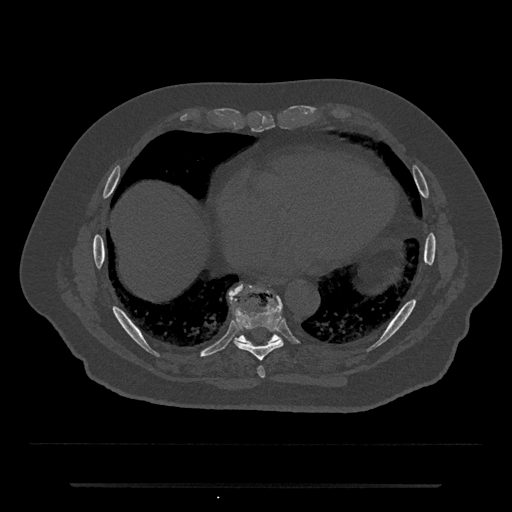
CT including the spine, one axial slice. Reconstruction kernel Br40s/3. 120 kVp. Bone window (W 1800 / L 400 HU). 512 × 512 image matrix, field of view 434 × 434 mm. Patient: male, 80 years. From the clinical record (not read from this slice): primary cancer: prostate.
Annotated regions visible in this slice (semi-automatically segmented with operator editing):
- T8 vertebra: bounding box [x1, y1, x2, y2] px = [233, 302, 283, 361]
- T9 vertebra: [229, 284, 281, 347]